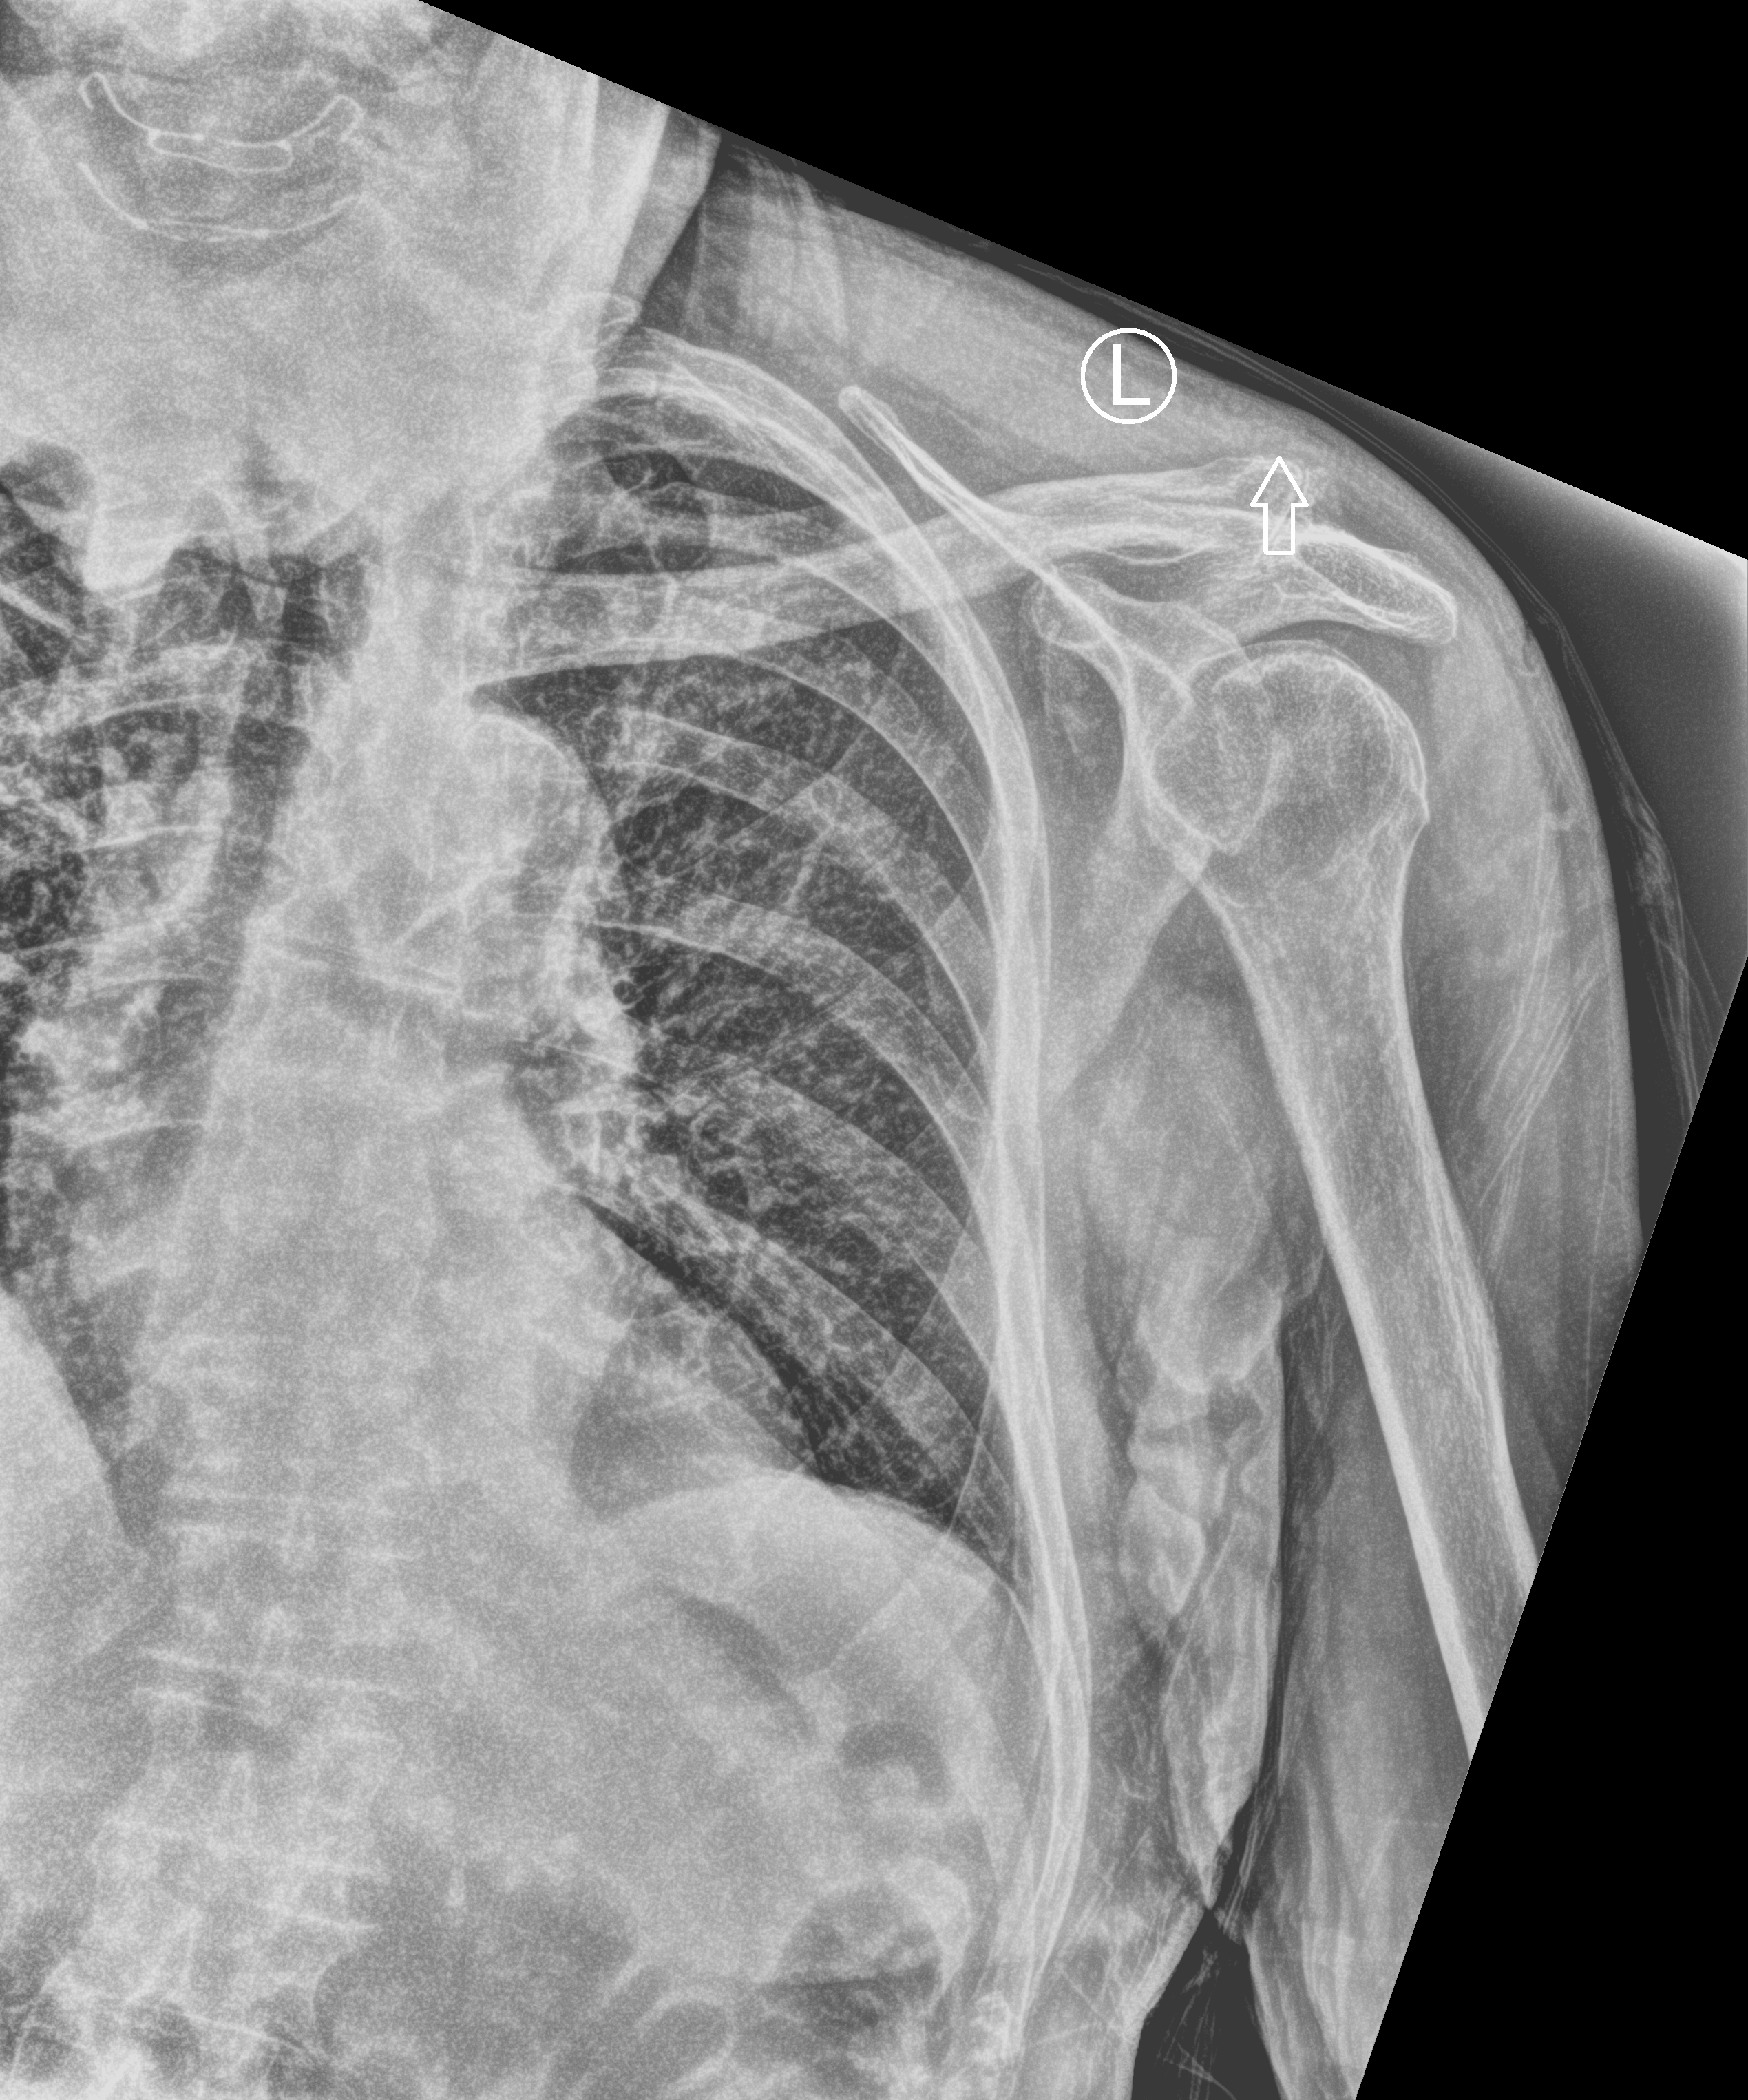
Portable chest radiograph; anteroposterior (AP) projection. Patient hospitalised with COVID-19; male, aged 75–90 years.
Admission-level facts for this patient (not findings on this image; timing relative to this image not recorded):
- admitted to intensive care during this hospital stay: yes